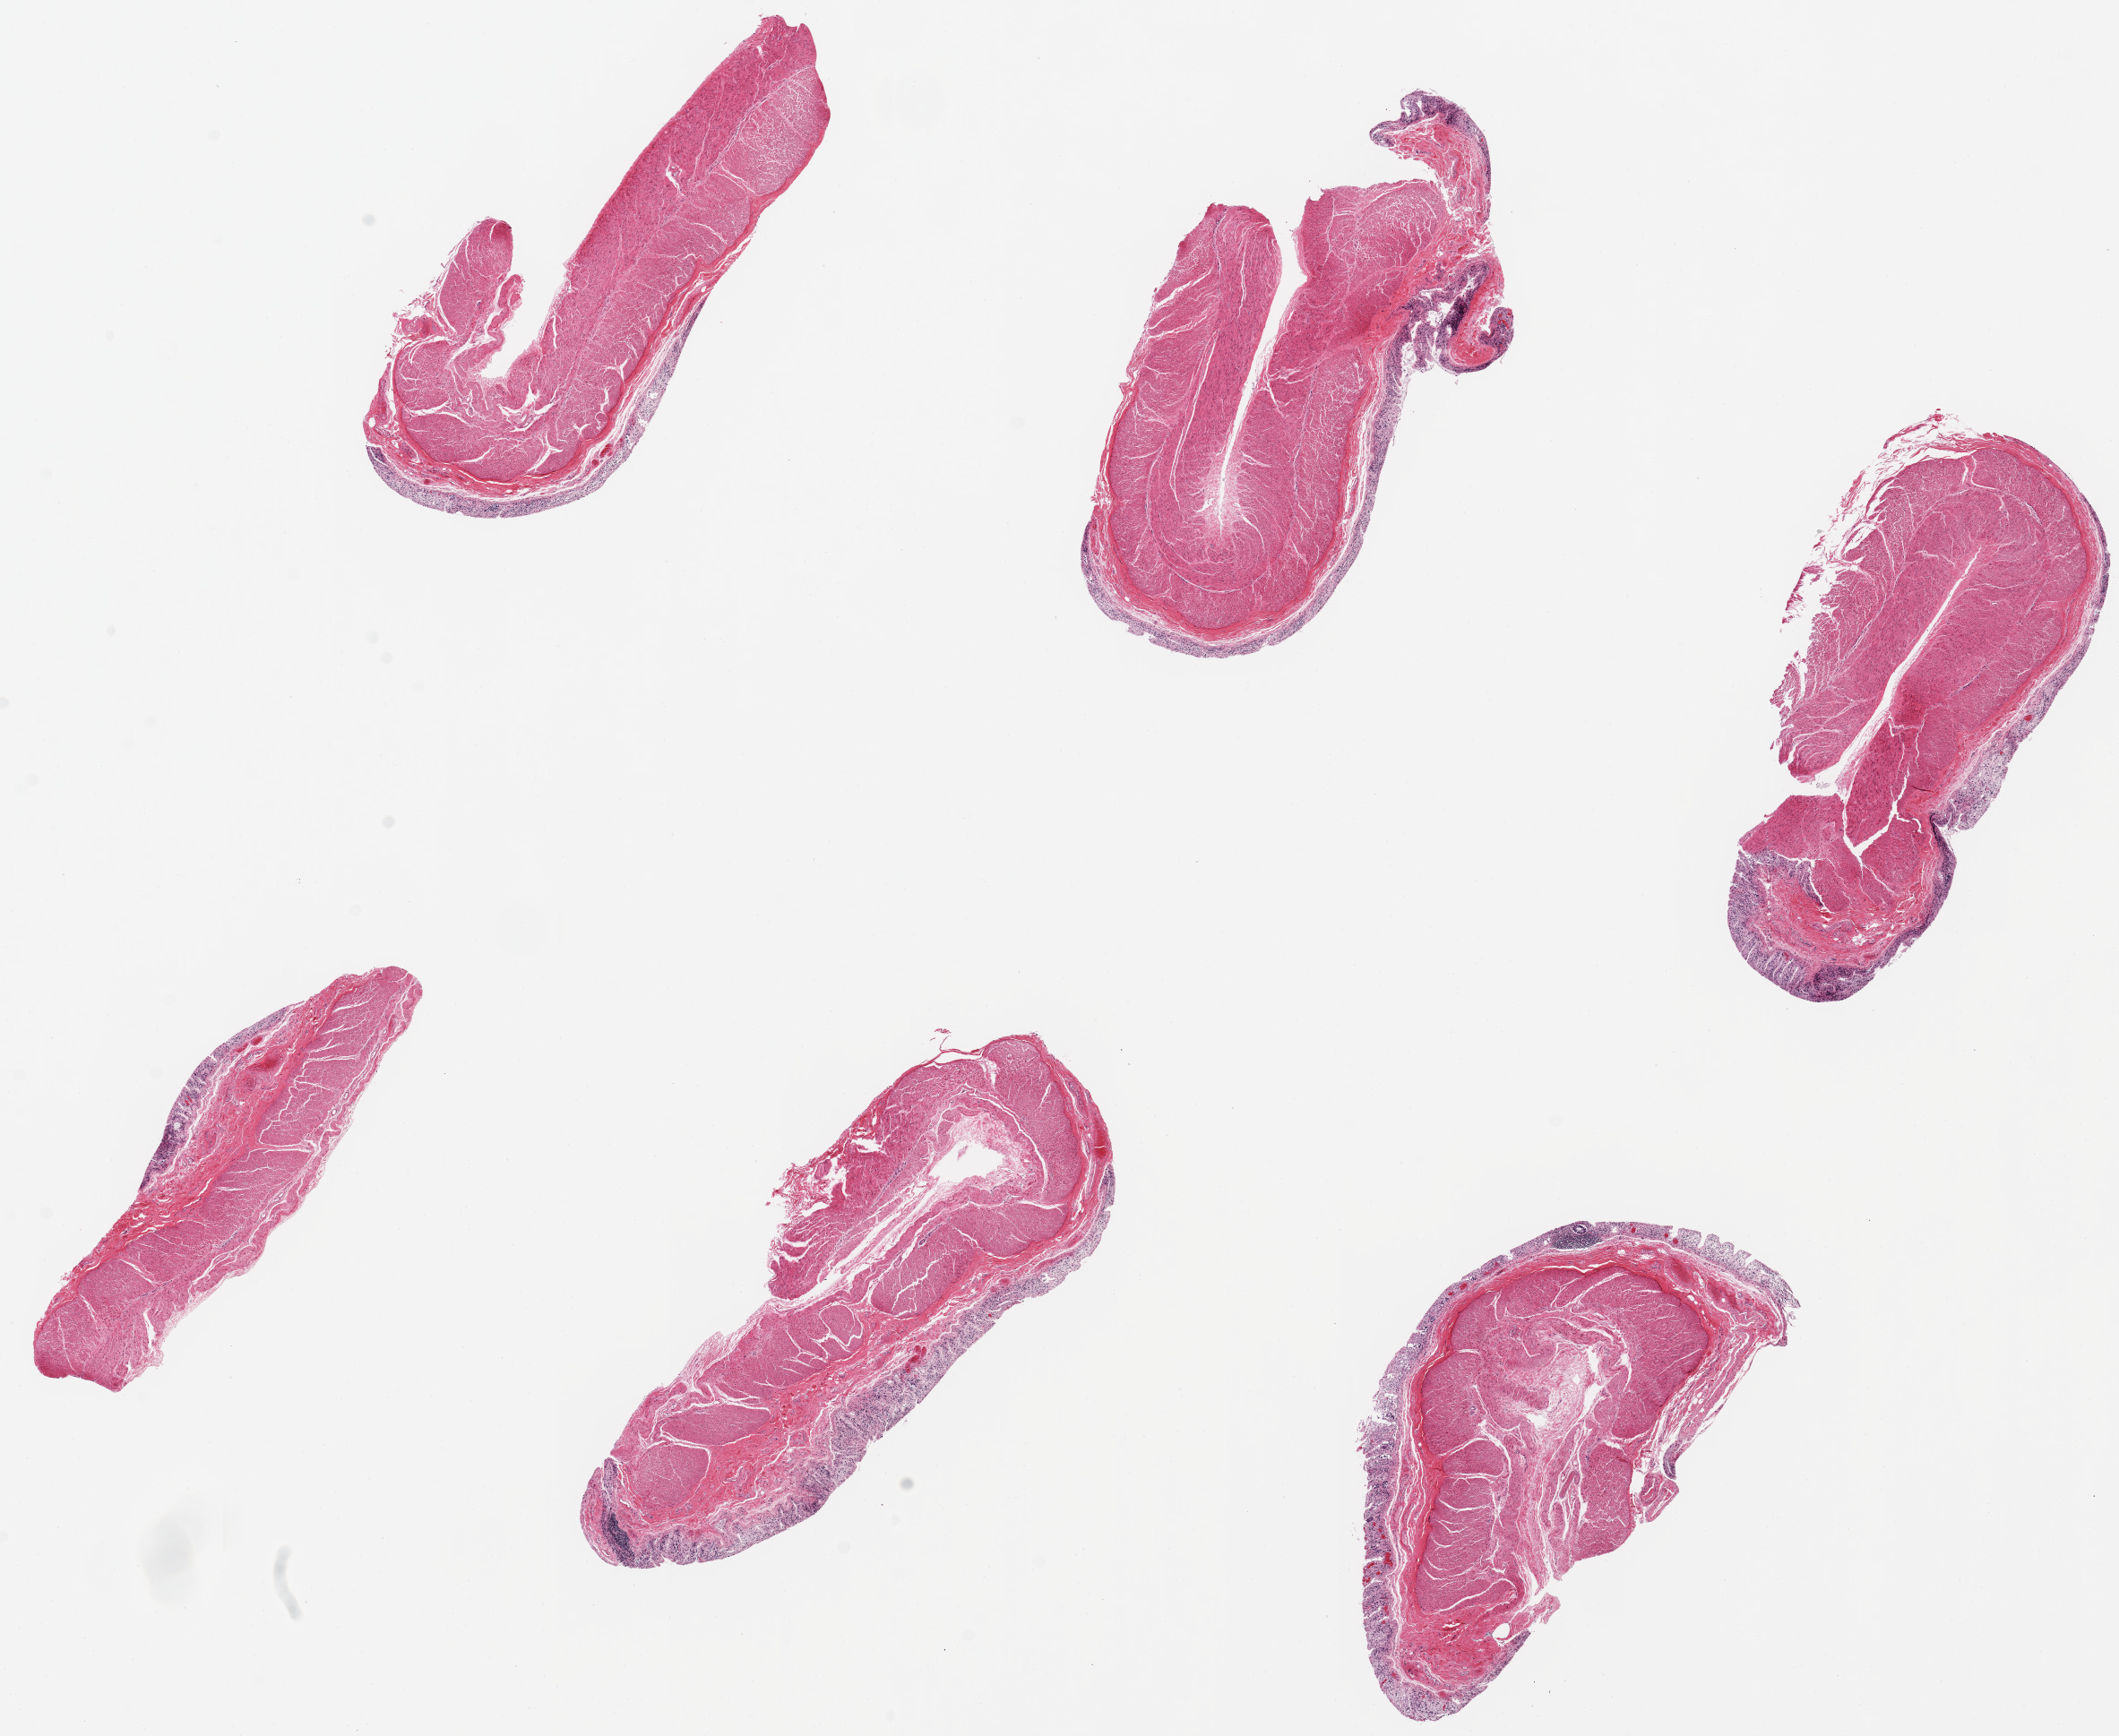
Digitized H&E-stained section — whole scanned area (about 18.7 x 15.3 mm, acquisition: 20x scan) shown as a low-resolution overview; PAXgene-fixed paraffin-embedded (PFPE) section; section of transverse colon (target tissue); donor tissue sample.
Pathologist's review note for this sample: 6 pieces, up to 6x2.5mm; mucosa=3; muscle =1.